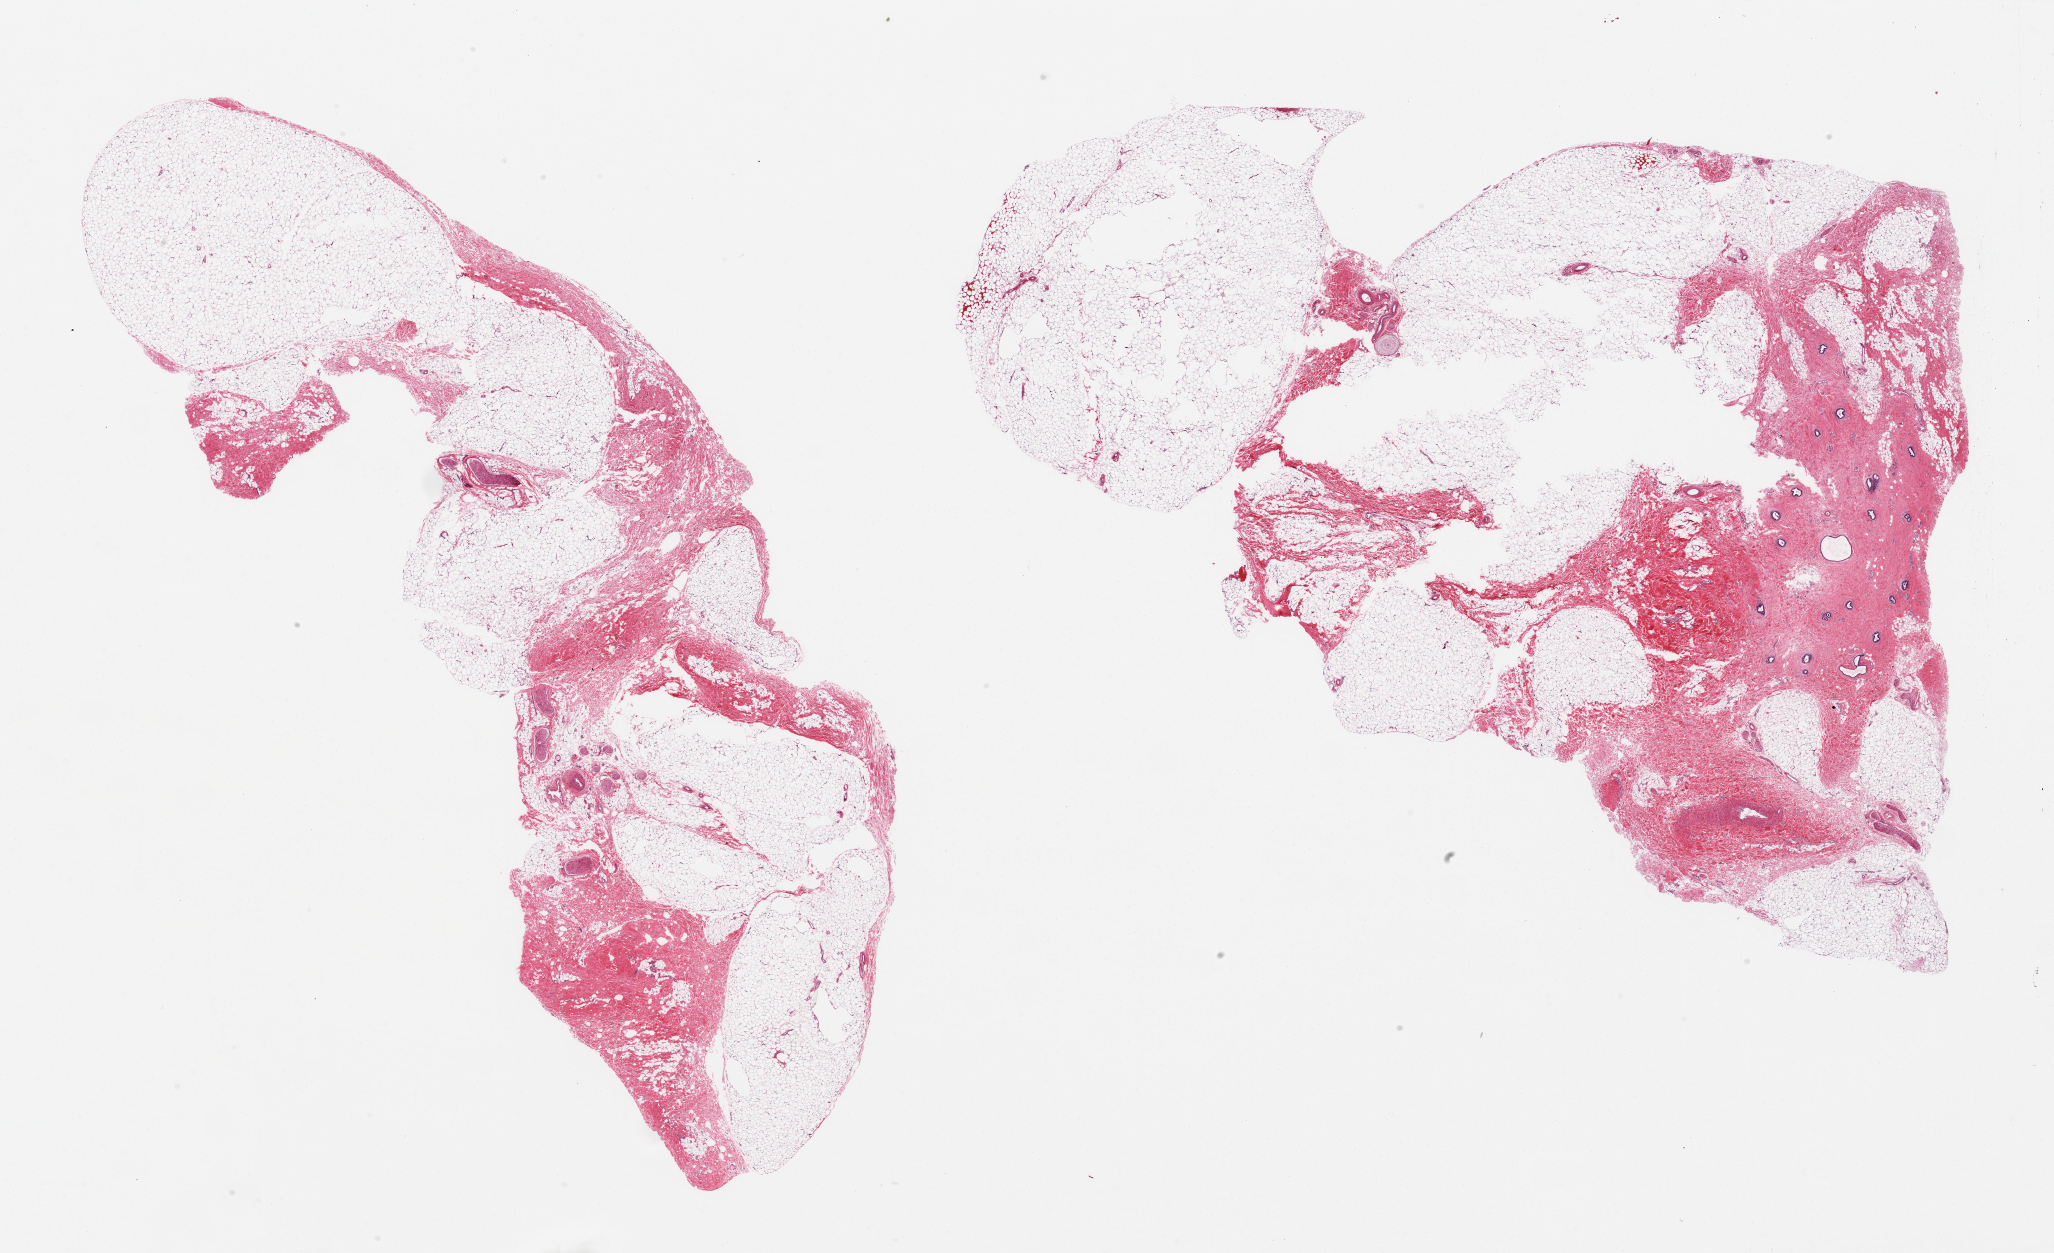
Digitized H&E-stained section, brightfield, whole scanned area (about 32.5 x 19.8 mm) shown as a low-resolution overview, PAXgene-fixed, paraffin-embedded tissue, section of breast (target tissue), tissue donor sample. Donor sex: male.
Pathologist's review note for this sample: 2 aliquots, ~18x9mm; Male ductal units well-seen in one, examples.